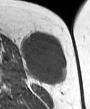
MRI of an extremity soft-tissue mass, one axial slice; MR volume resampled by the dataset authors to the PET/CT grid (not the native acquisition matrix); 90 × 109 image matrix, field of view 88 × 106 mm. Female patient. From the clinical record (not read from this slice): histological type: leiomyosarcoma; grade: intermediate; site of the primary tumour: parascapusular.
Annotated regions visible in this slice (expert contour drawn on MRI and transferred to this co-registered scan by the dataset authors):
- gross tumour volume including surrounding oedema: bounding box <21,32,66,85> (left, top, right, bottom; pixels)
- gross tumour volume (mass): <21,32,66,85>